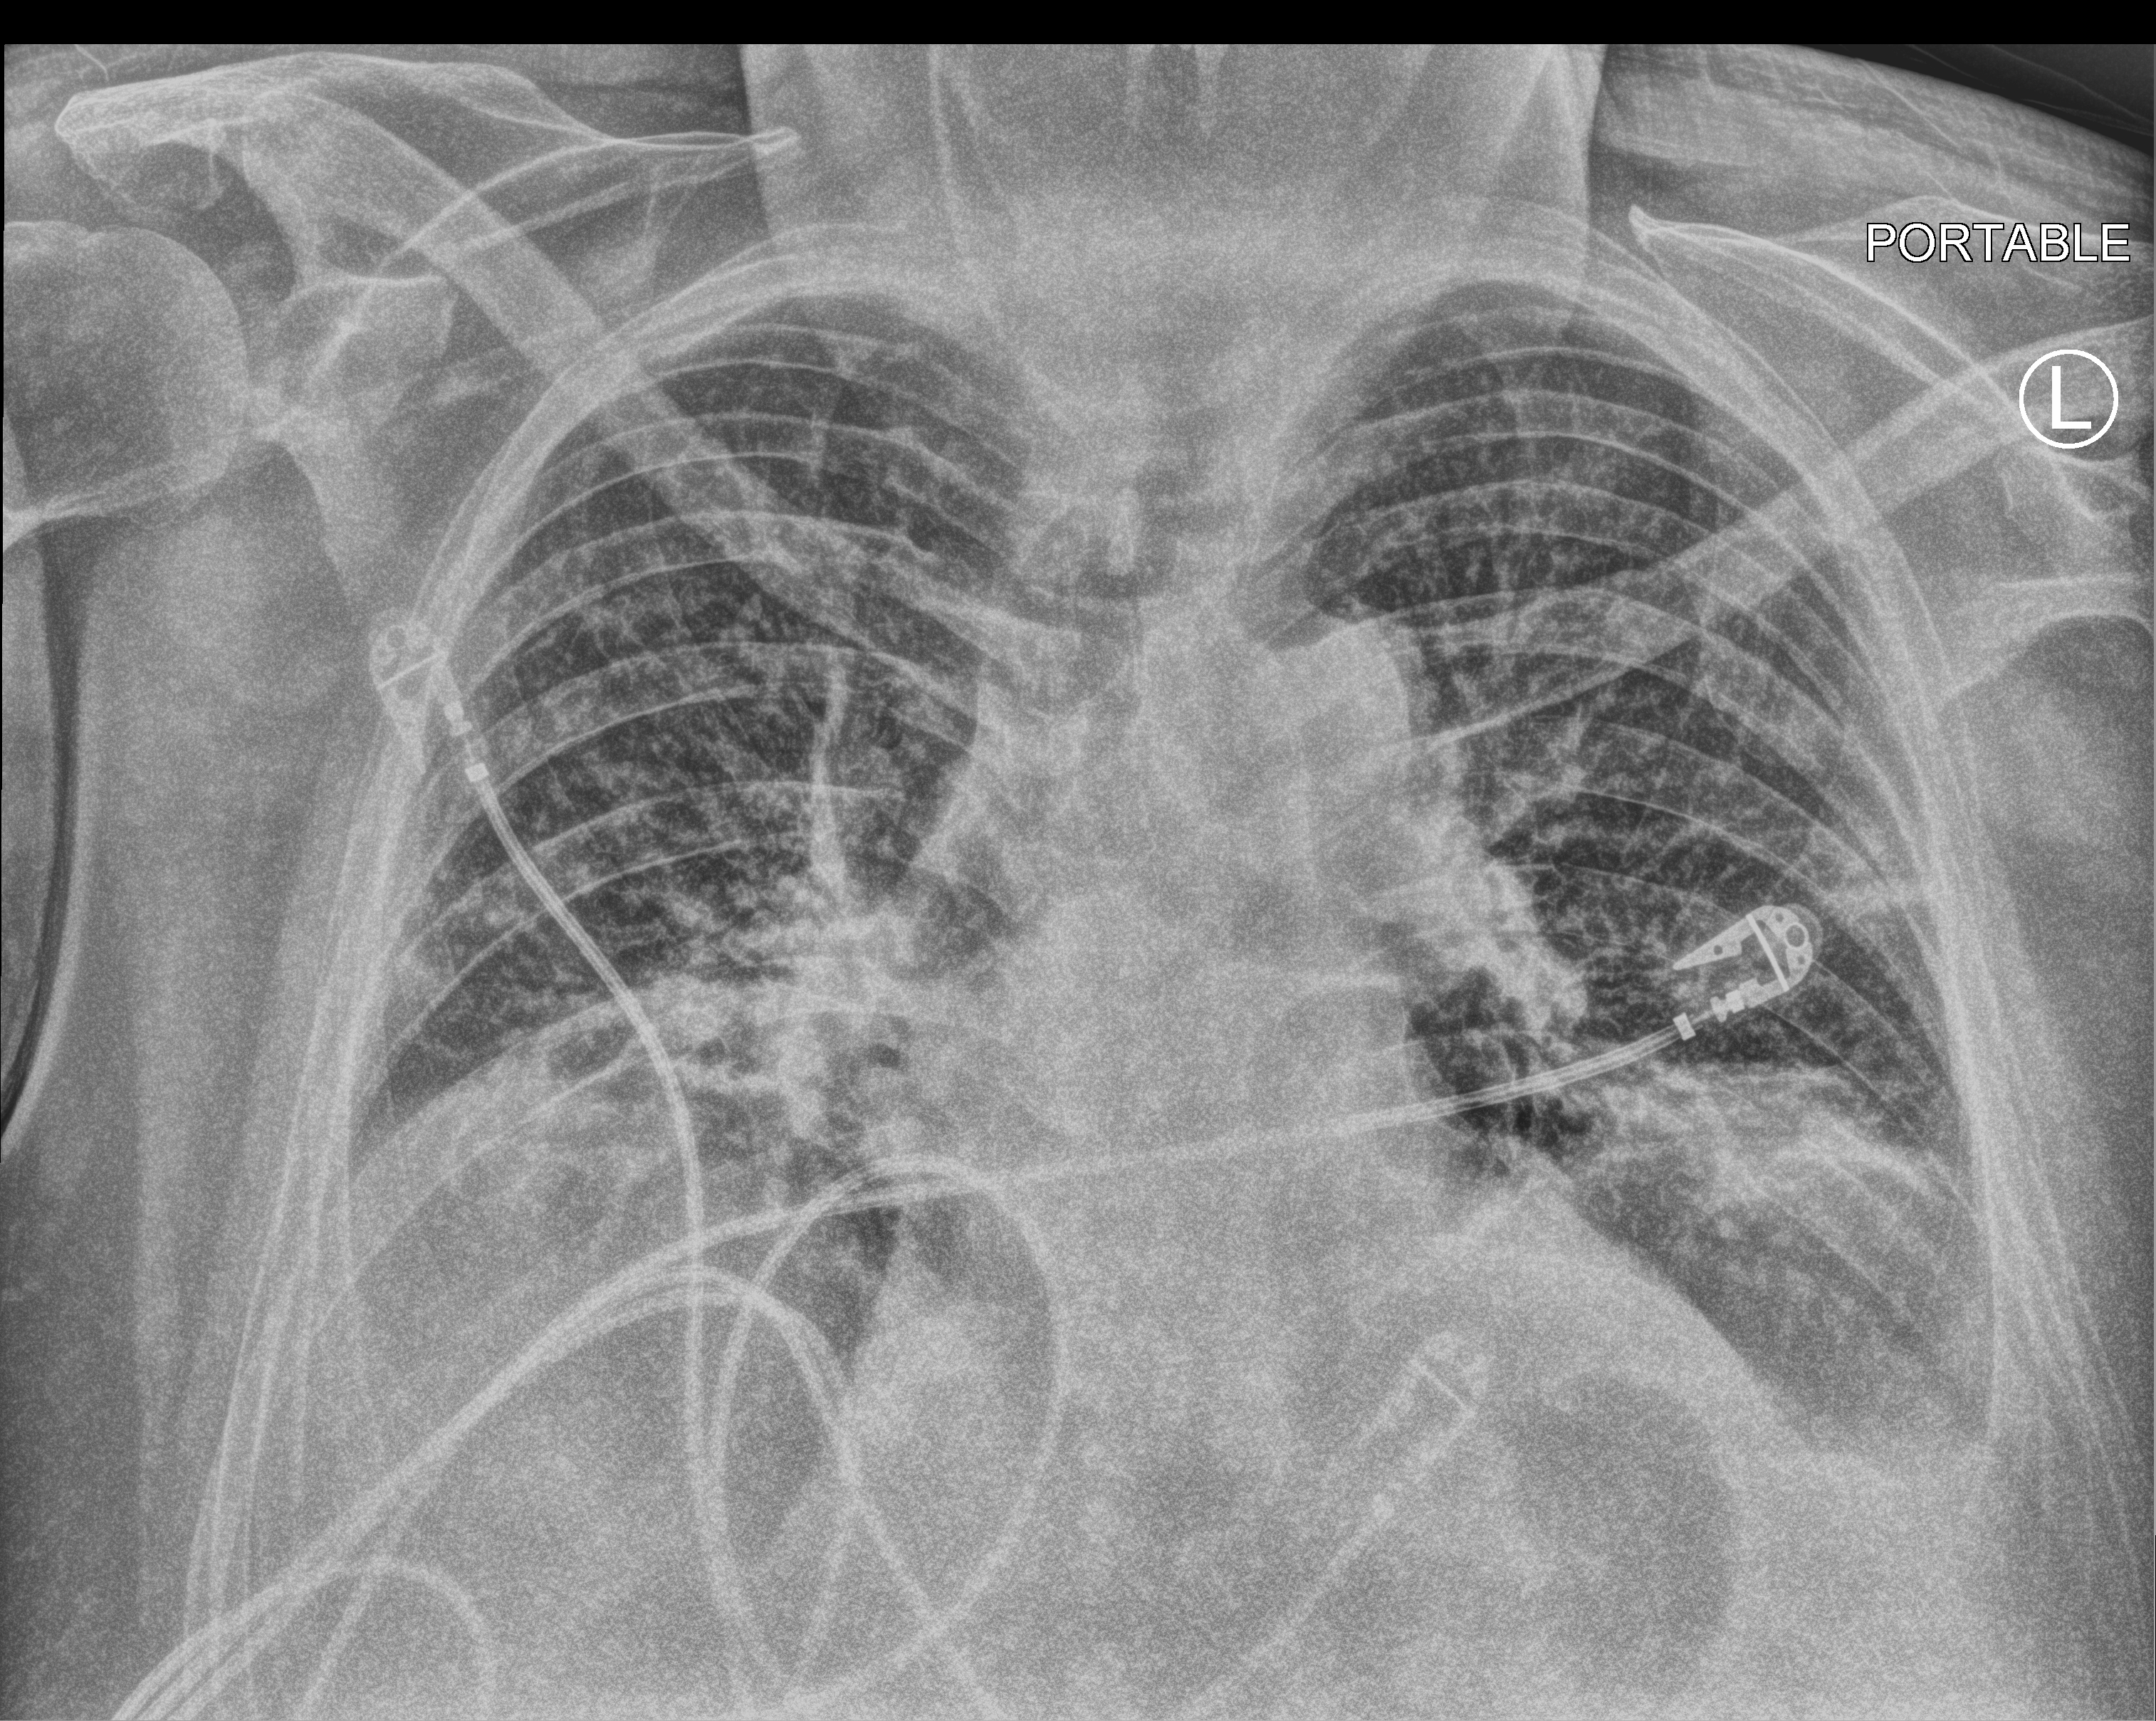
Bedside chest radiograph (computed radiography), anteroposterior (AP) projection. Male patient hospitalised with COVID-19, age 60–74 years.
From the hospital-stay record, not from the radiograph (when in the stay this image was taken is not recorded): admitted to intensive care during this hospital stay: yes; mechanically ventilated during this hospital stay: yes.